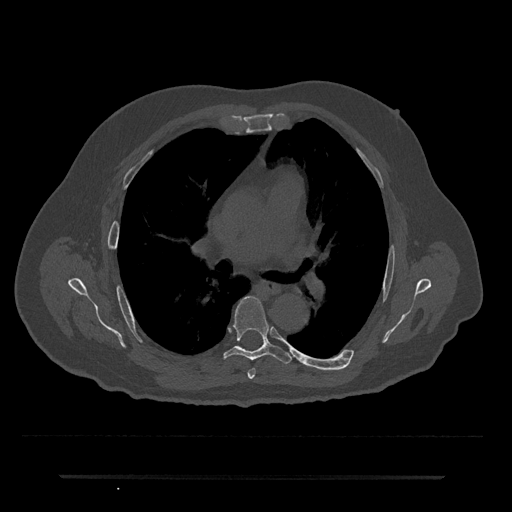
CT including the spine, one axial slice; slice 441 of 797 in the series (ordered by position); 120 kVp; bone window (W 1800 / L 400 HU); 0.5 mm slice thickness; 512 × 512 image matrix. Patient: male, 69 years. Case-level facts recorded for this patient, not image findings: primary cancer: prostate.
Structures marked on this image (semi-automatically segmented with operator editing):
- T5 vertebra: box from (x=248, y=368) to (x=255, y=379) px
- T6 vertebra: (x=224, y=297)–(x=292, y=364)